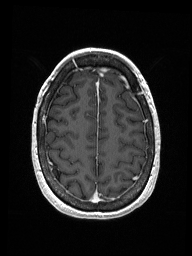
Brain MRI from a brain-tumour surgery series, one axial slice. Slice 43 of 192 in the series (ordered by position). T1-weighted post-contrast. 1 mm slice thickness. 192 × 256 image matrix. From the clinical record (not read from this slice): histopathology: Metastastic Carcinoma from Breast primary; tumour location: Right Frontal.
Outlined on this slice (outlined manually by an expert reader):
- previous resection cavity: bounding box (x1, y1, x2, y2) in pixels: (102, 69, 107, 70)